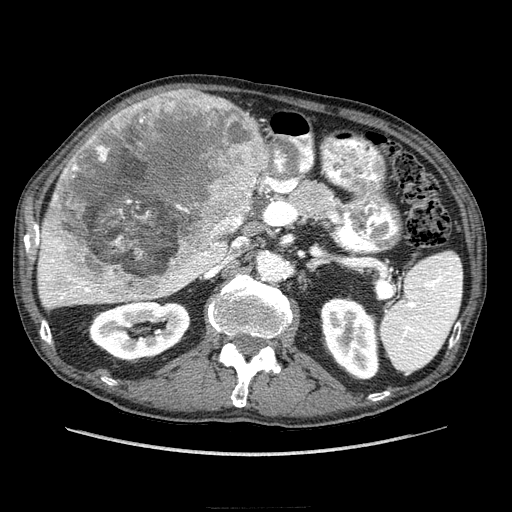
Contrast-enhanced abdominal CT (liver protocol), one axial slice; position 129 of 218 along the scan axis; soft-tissue window (W 400 / L 40 HU); 2.5 mm slice thickness; 512 × 512 image matrix, field of view 380 × 380 mm. Case-level facts recorded for this patient, not image findings: diagnosis: hepatocellular carcinoma (patient treated with transarterial chemoembolisation; whether this scan precedes or follows treatment is not stated here); TNM stage (as recorded): Stage-IIIA; Child-Pugh class: A.
Annotated regions visible in this slice (semi-automatically segmented with operator editing):
- liver parenchyma outside the tumour (the mass and vessels are separate outlines, so this box may not span the whole liver): bounding box (x1, y1, x2, y2) in pixels: (38, 100, 268, 308)
- mass: (41, 88, 268, 297)
- liver vessels: (41, 263, 186, 303)